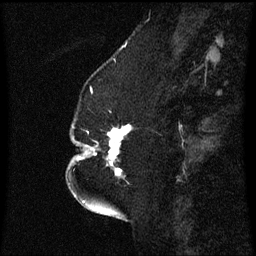
Breast MRI (dynamic contrast-enhanced), one sagittal slice. Dynamic contrast-enhanced series, image 2 of 3 at this slice position (ordered by acquisition). 1.5 T. TE 4.2 ms, TR 8.4 ms. 2.3 mm slice thickness. 256 × 256 image matrix, field of view 200 × 200 mm. Female patient, age 52 years. Case-level facts recorded for this patient, not image findings: setting: breast cancer imaged before/during neoadjuvant chemotherapy; receptor status: HR-positive, HER2-negative.
Outlined on this slice (semi-automatic segmentation, software-assisted and operator-edited):
- analysis volume of interest (the breast-tissue region the enhancement analysis was run in; not a lesion): box from (x=75, y=118) to (x=131, y=181) px
- tumour enhancement mask (voxels above the 70 % enhancement threshold inside the analysis volume of interest): (x=77, y=126)–(x=130, y=177)